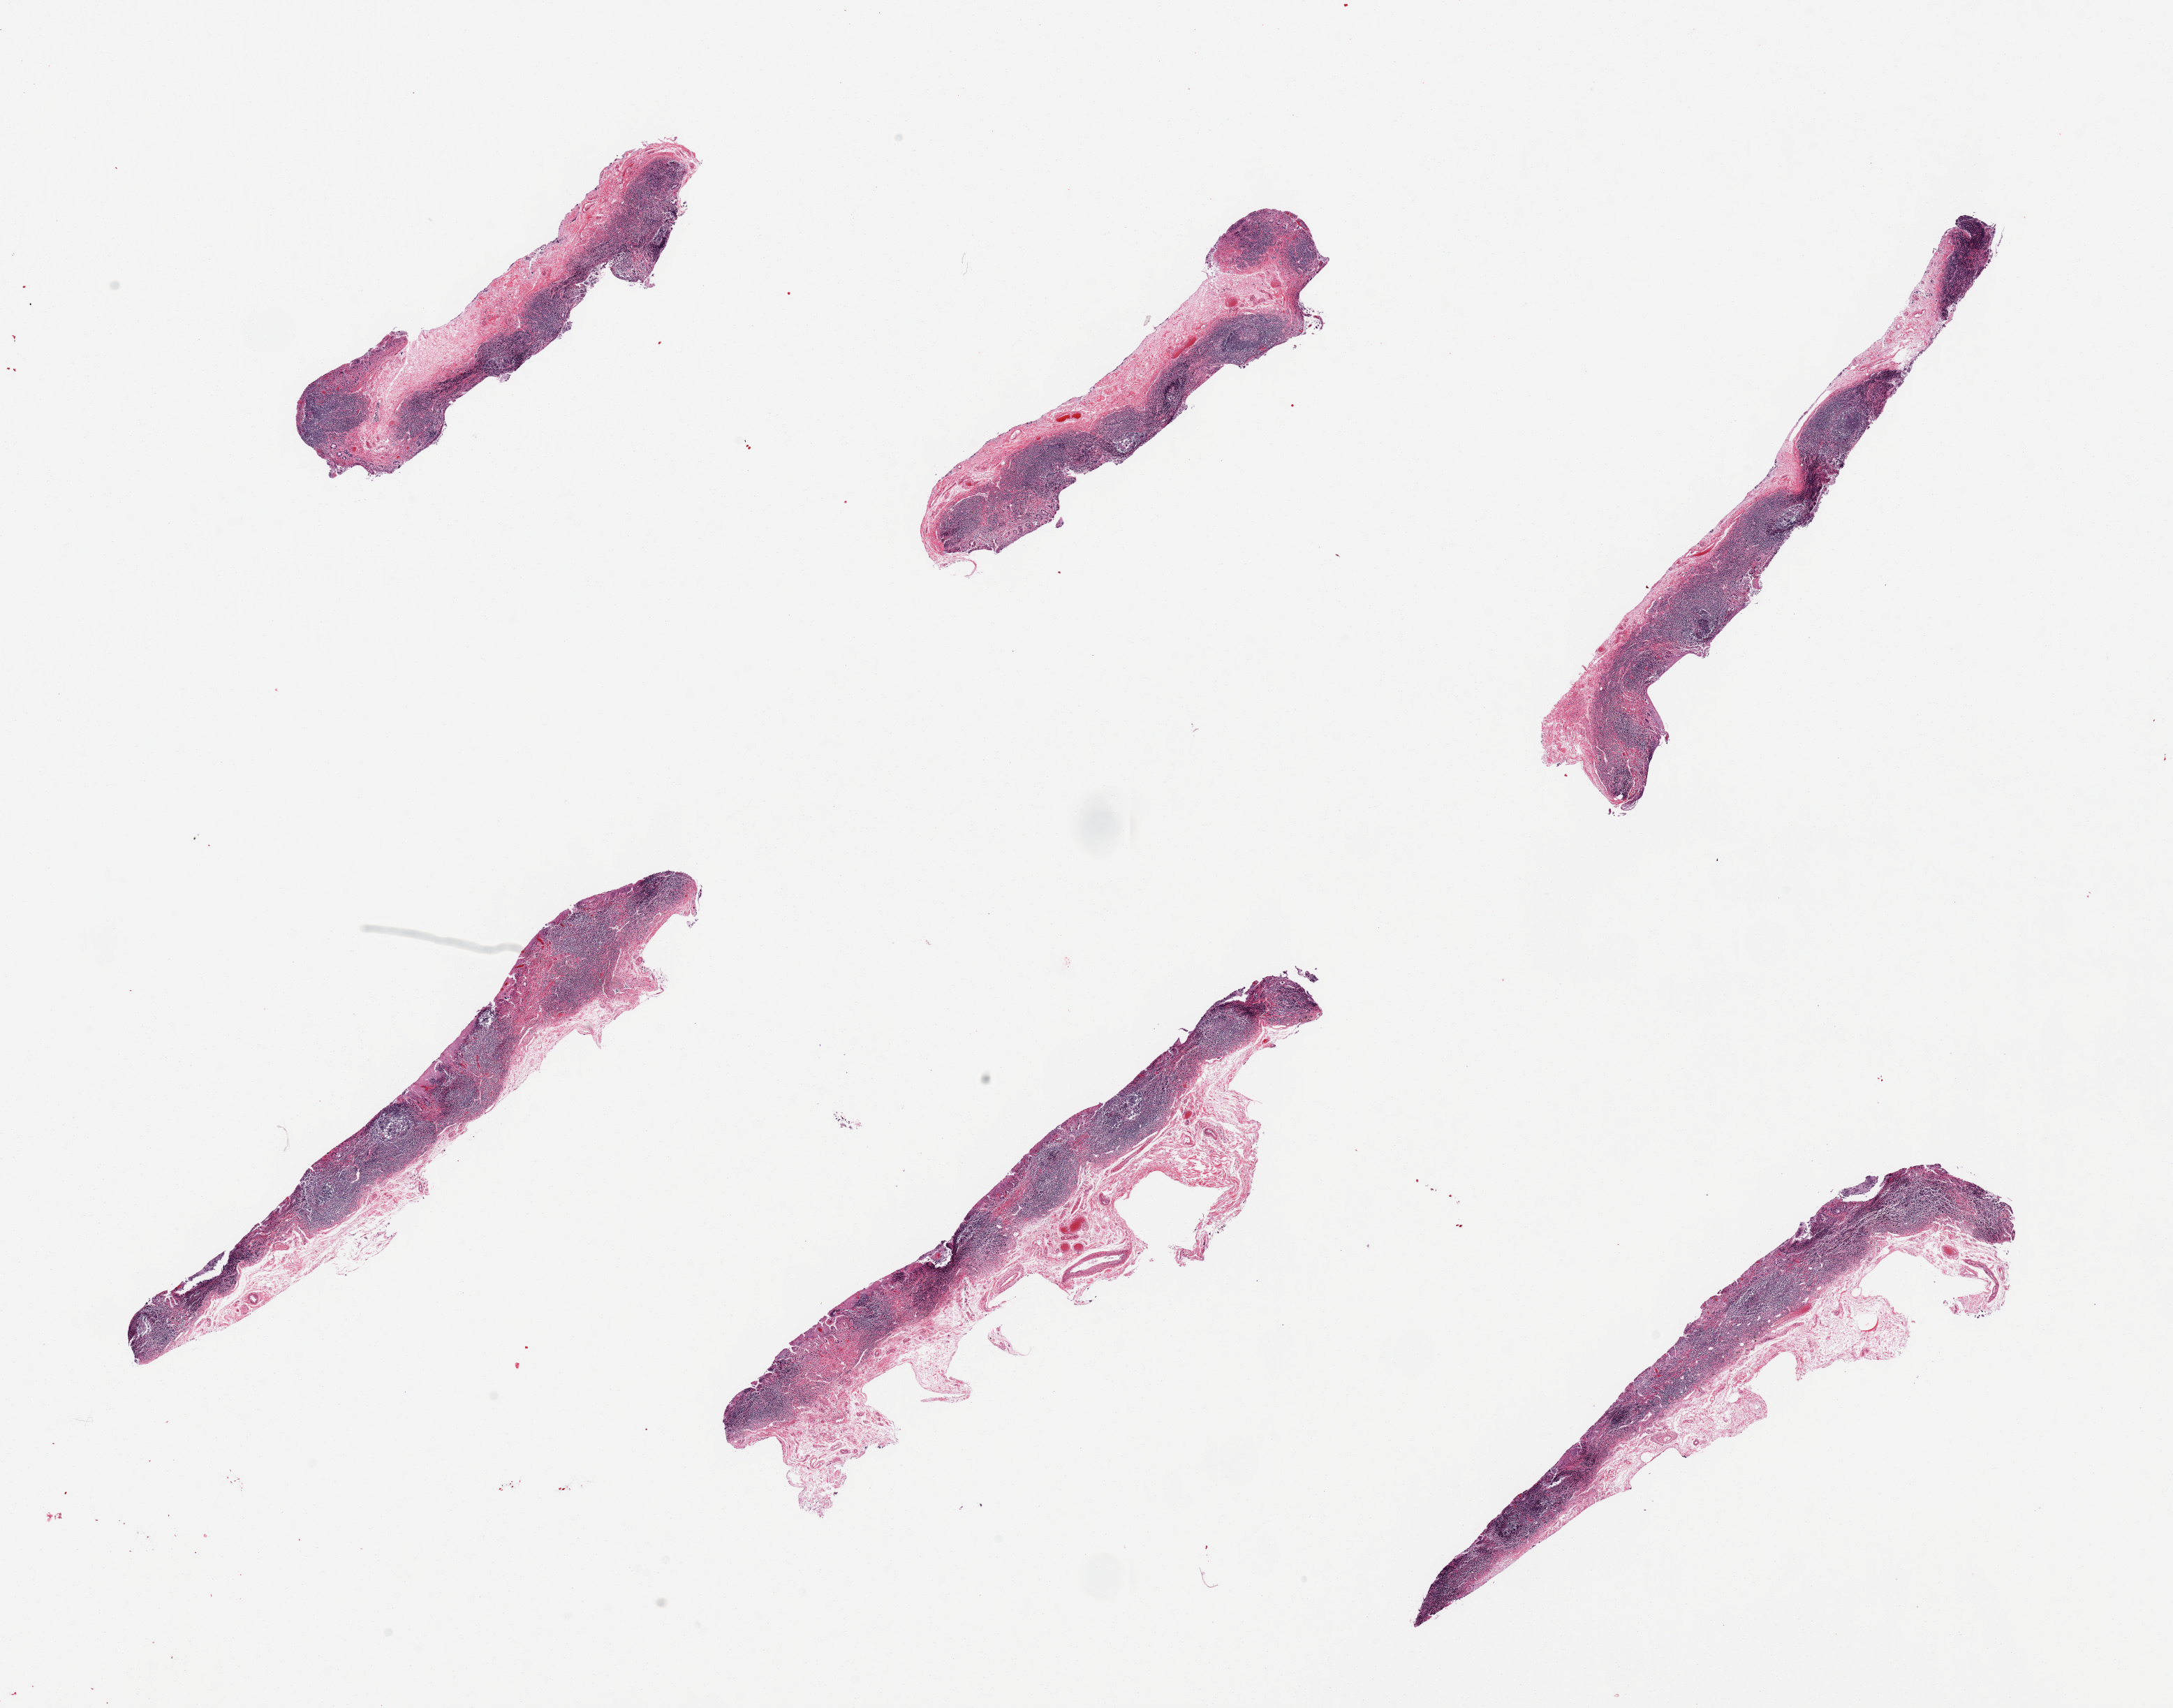
Haematoxylin and eosin whole-slide image, brightfield, shown as a low-resolution overview of the whole scanned area (about 24.6 x 19.3 mm); PAXgene-fixed, paraffin-embedded tissue; sampled site (target tissue): ileum; tissue donor sample. Donor sex: male.
Review note (as recorded): 6 pieces, lympohoid aggregates are ~50% of tissue.